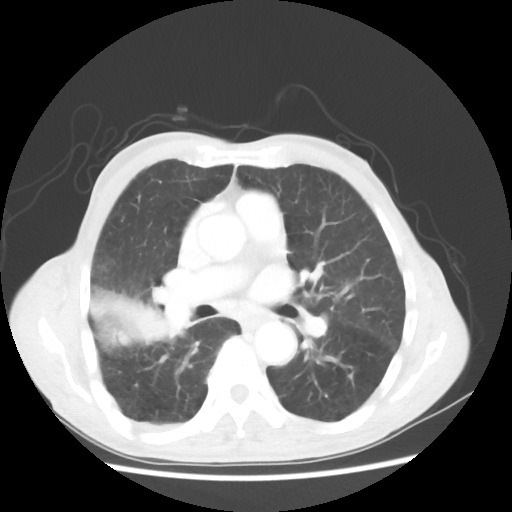
Chest CT, one axial slice. Position 30 of 58 along the scan axis. Reconstruction kernel STANDARD. 100 kVp. Lung window (W 1500 / L -600 HU). 5 mm slice thickness. 512 × 512 image matrix, field of view 351 × 351 mm. Male patient, age 75 years. Case-level facts recorded for this patient, not image findings: clinical TNM (as recorded): T4 N1 M1.
Structures marked on this image (bounding box drawn by a radiologist):
- lung tumour (recorded histology: adenocarcinoma): bounding box <75,280,176,353> (left, top, right, bottom; pixels)